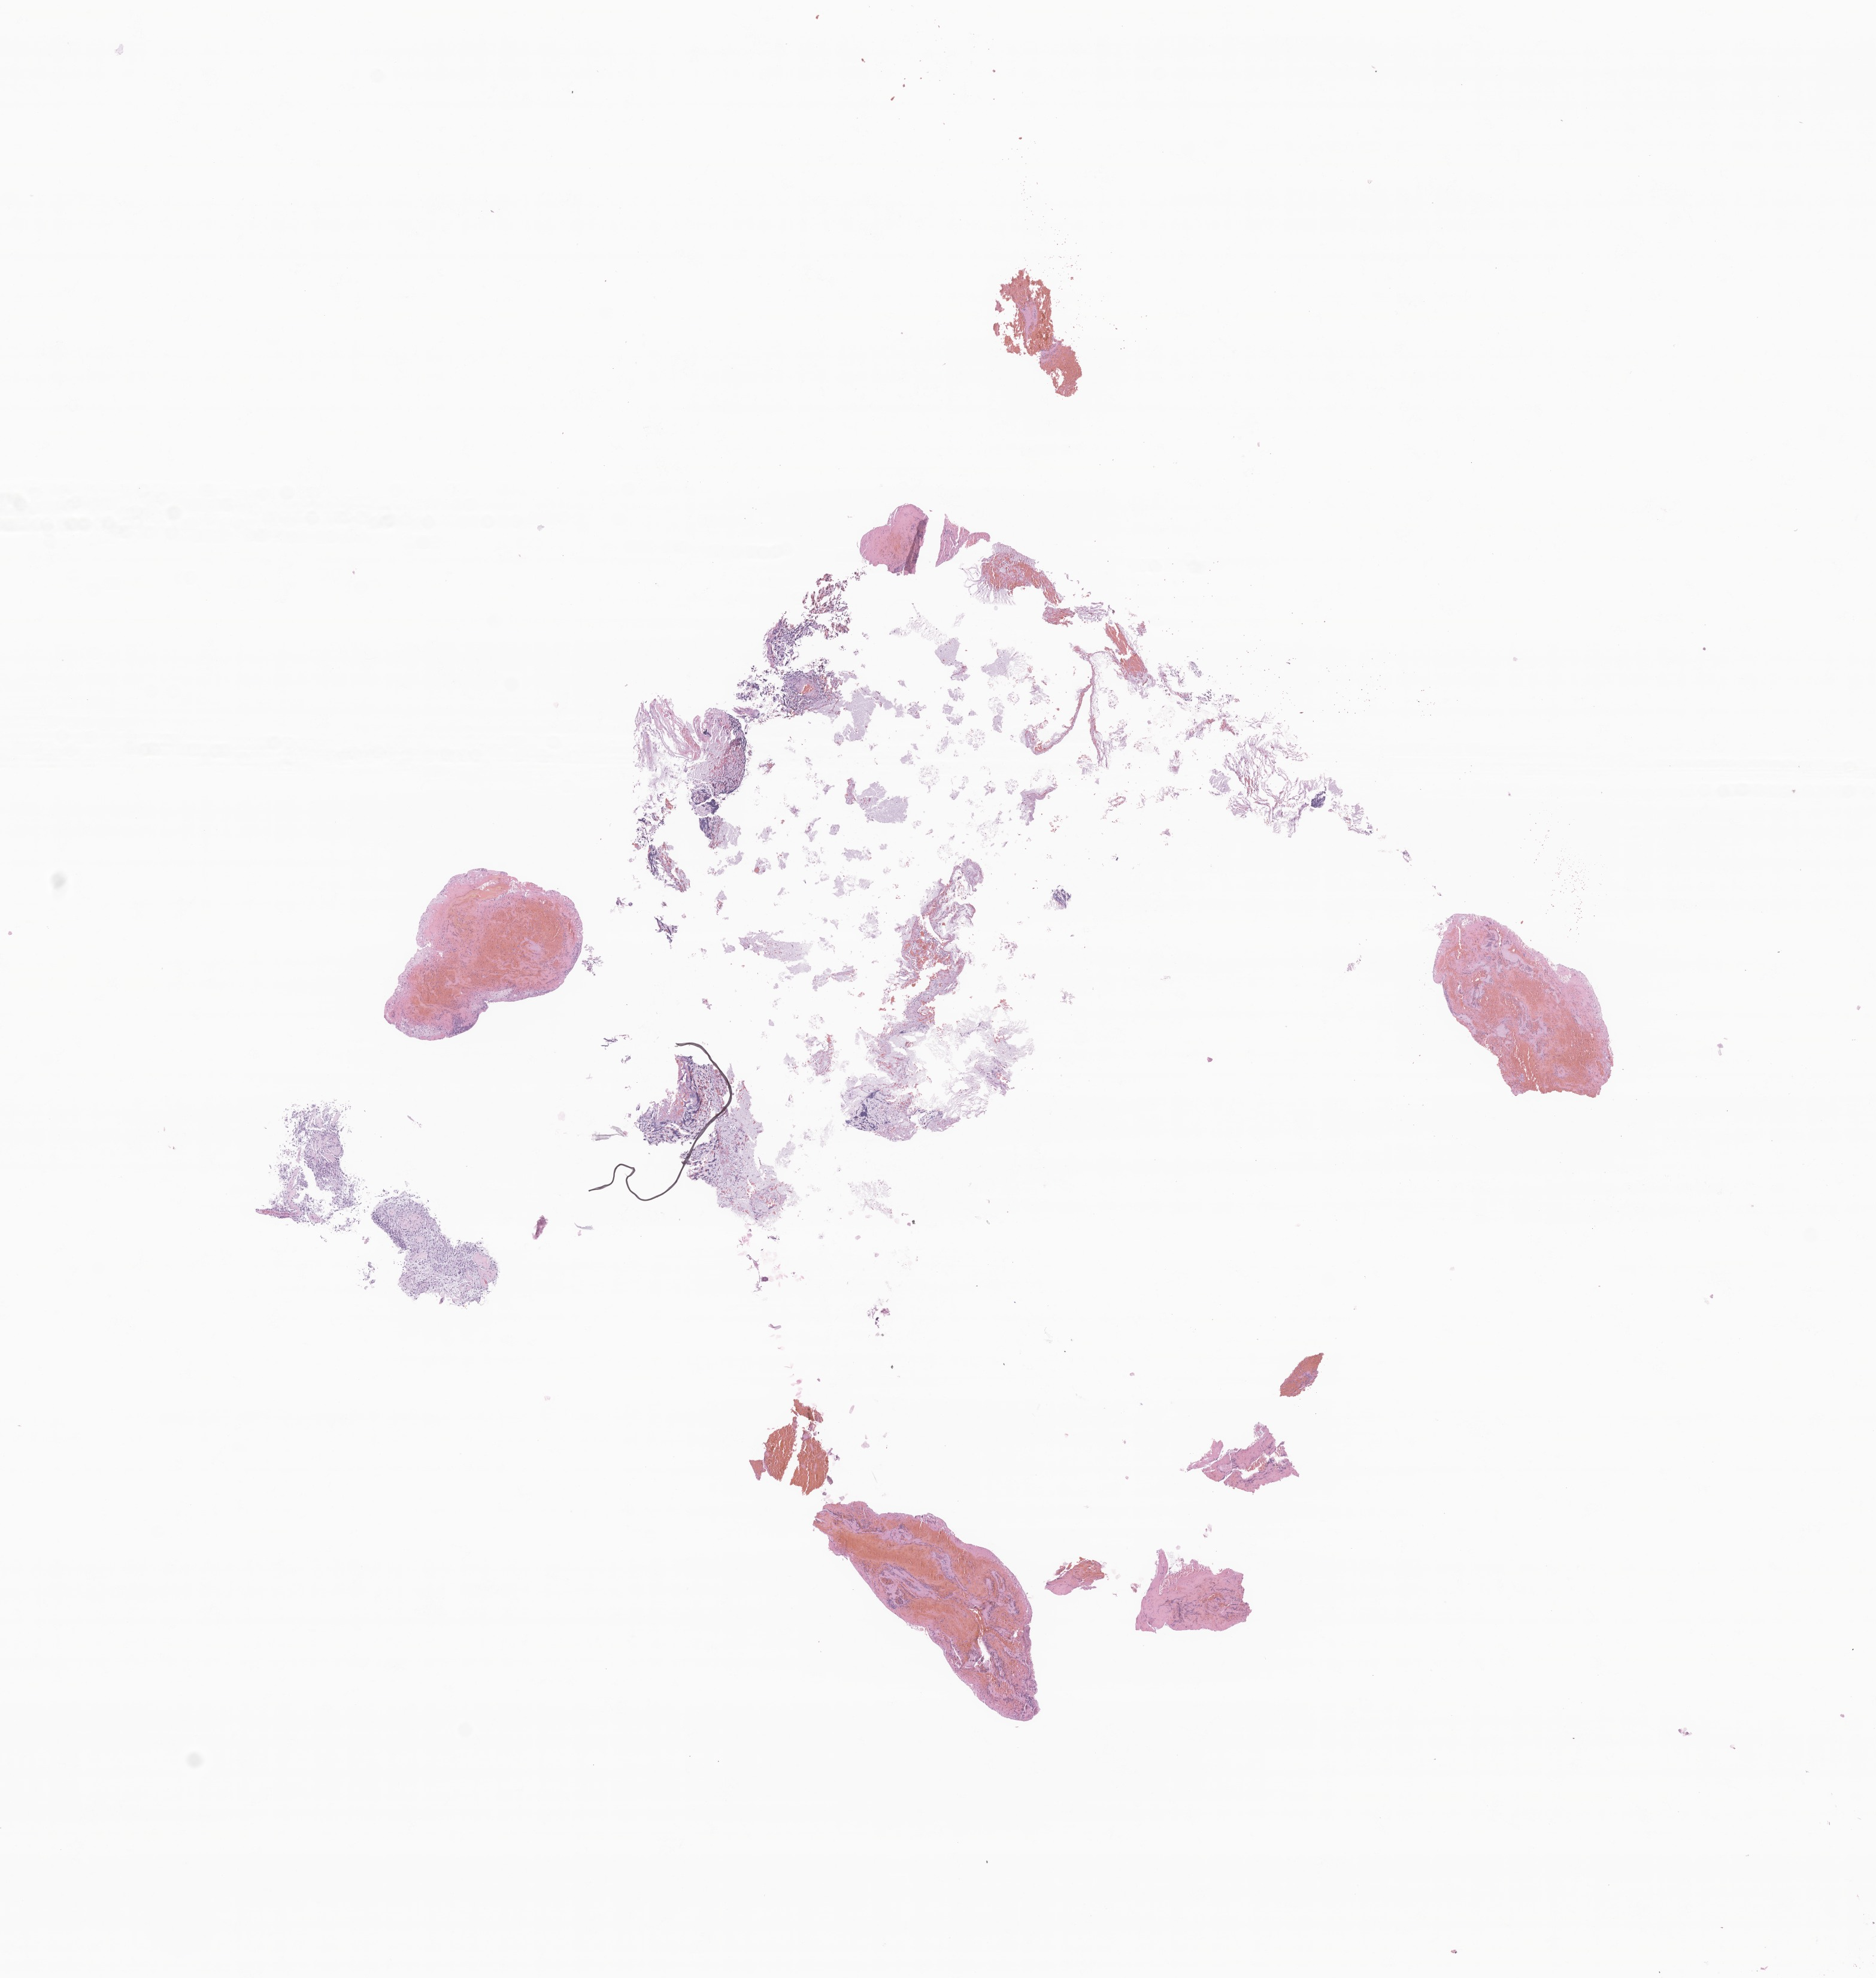
Digitized H&E-stained section of tumor tissue from the cerebral ventricle — a low-resolution overview of the entire scanned area, about 13.2 x 13.9 mm, FFPE section. Patient: female, age 105 months (8 years 9 months).
* diagnosis (ICD-O-3 morphology term): Pilocytic astrocytoma